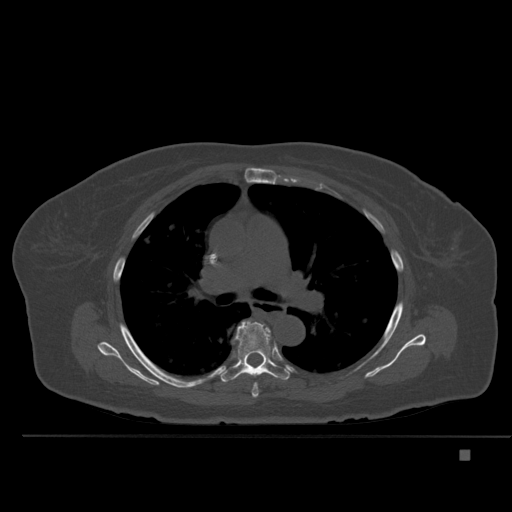
CT including the spine, one axial slice; position 343 of 477 along the scan axis; bone window (W 1800 / L 400 HU); 1.5 mm slice thickness; 512 × 512 image matrix. Patient: female, 74 years. Case-level facts recorded for this patient, not image findings: primary cancer: colon.
Structures marked on this image (semi-automatically segmented with operator editing):
- T5 vertebra: bounding box [x1, y1, x2, y2] px = [252, 383, 259, 399]
- T6 vertebra: [219, 321, 292, 382]